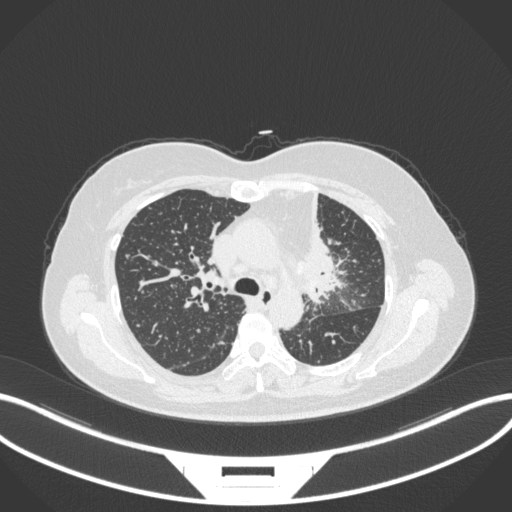
Chest CT, one axial slice; position 226 of 348 along the scan axis; reconstruction kernel B31f; 120 kVp; lung window (W 1500 / L -600 HU); 1 mm slice thickness; 512 × 512 image matrix, field of view 400 × 400 mm. Female patient, age 49 years. Case-level facts recorded for this patient, not image findings: clinical TNM (as recorded): T1c N0 M1.
Annotated regions visible in this slice (rectangle marked by the reading radiologist):
- lung tumour (recorded histology: adenocarcinoma): box from (x=290, y=186) to (x=347, y=308) px